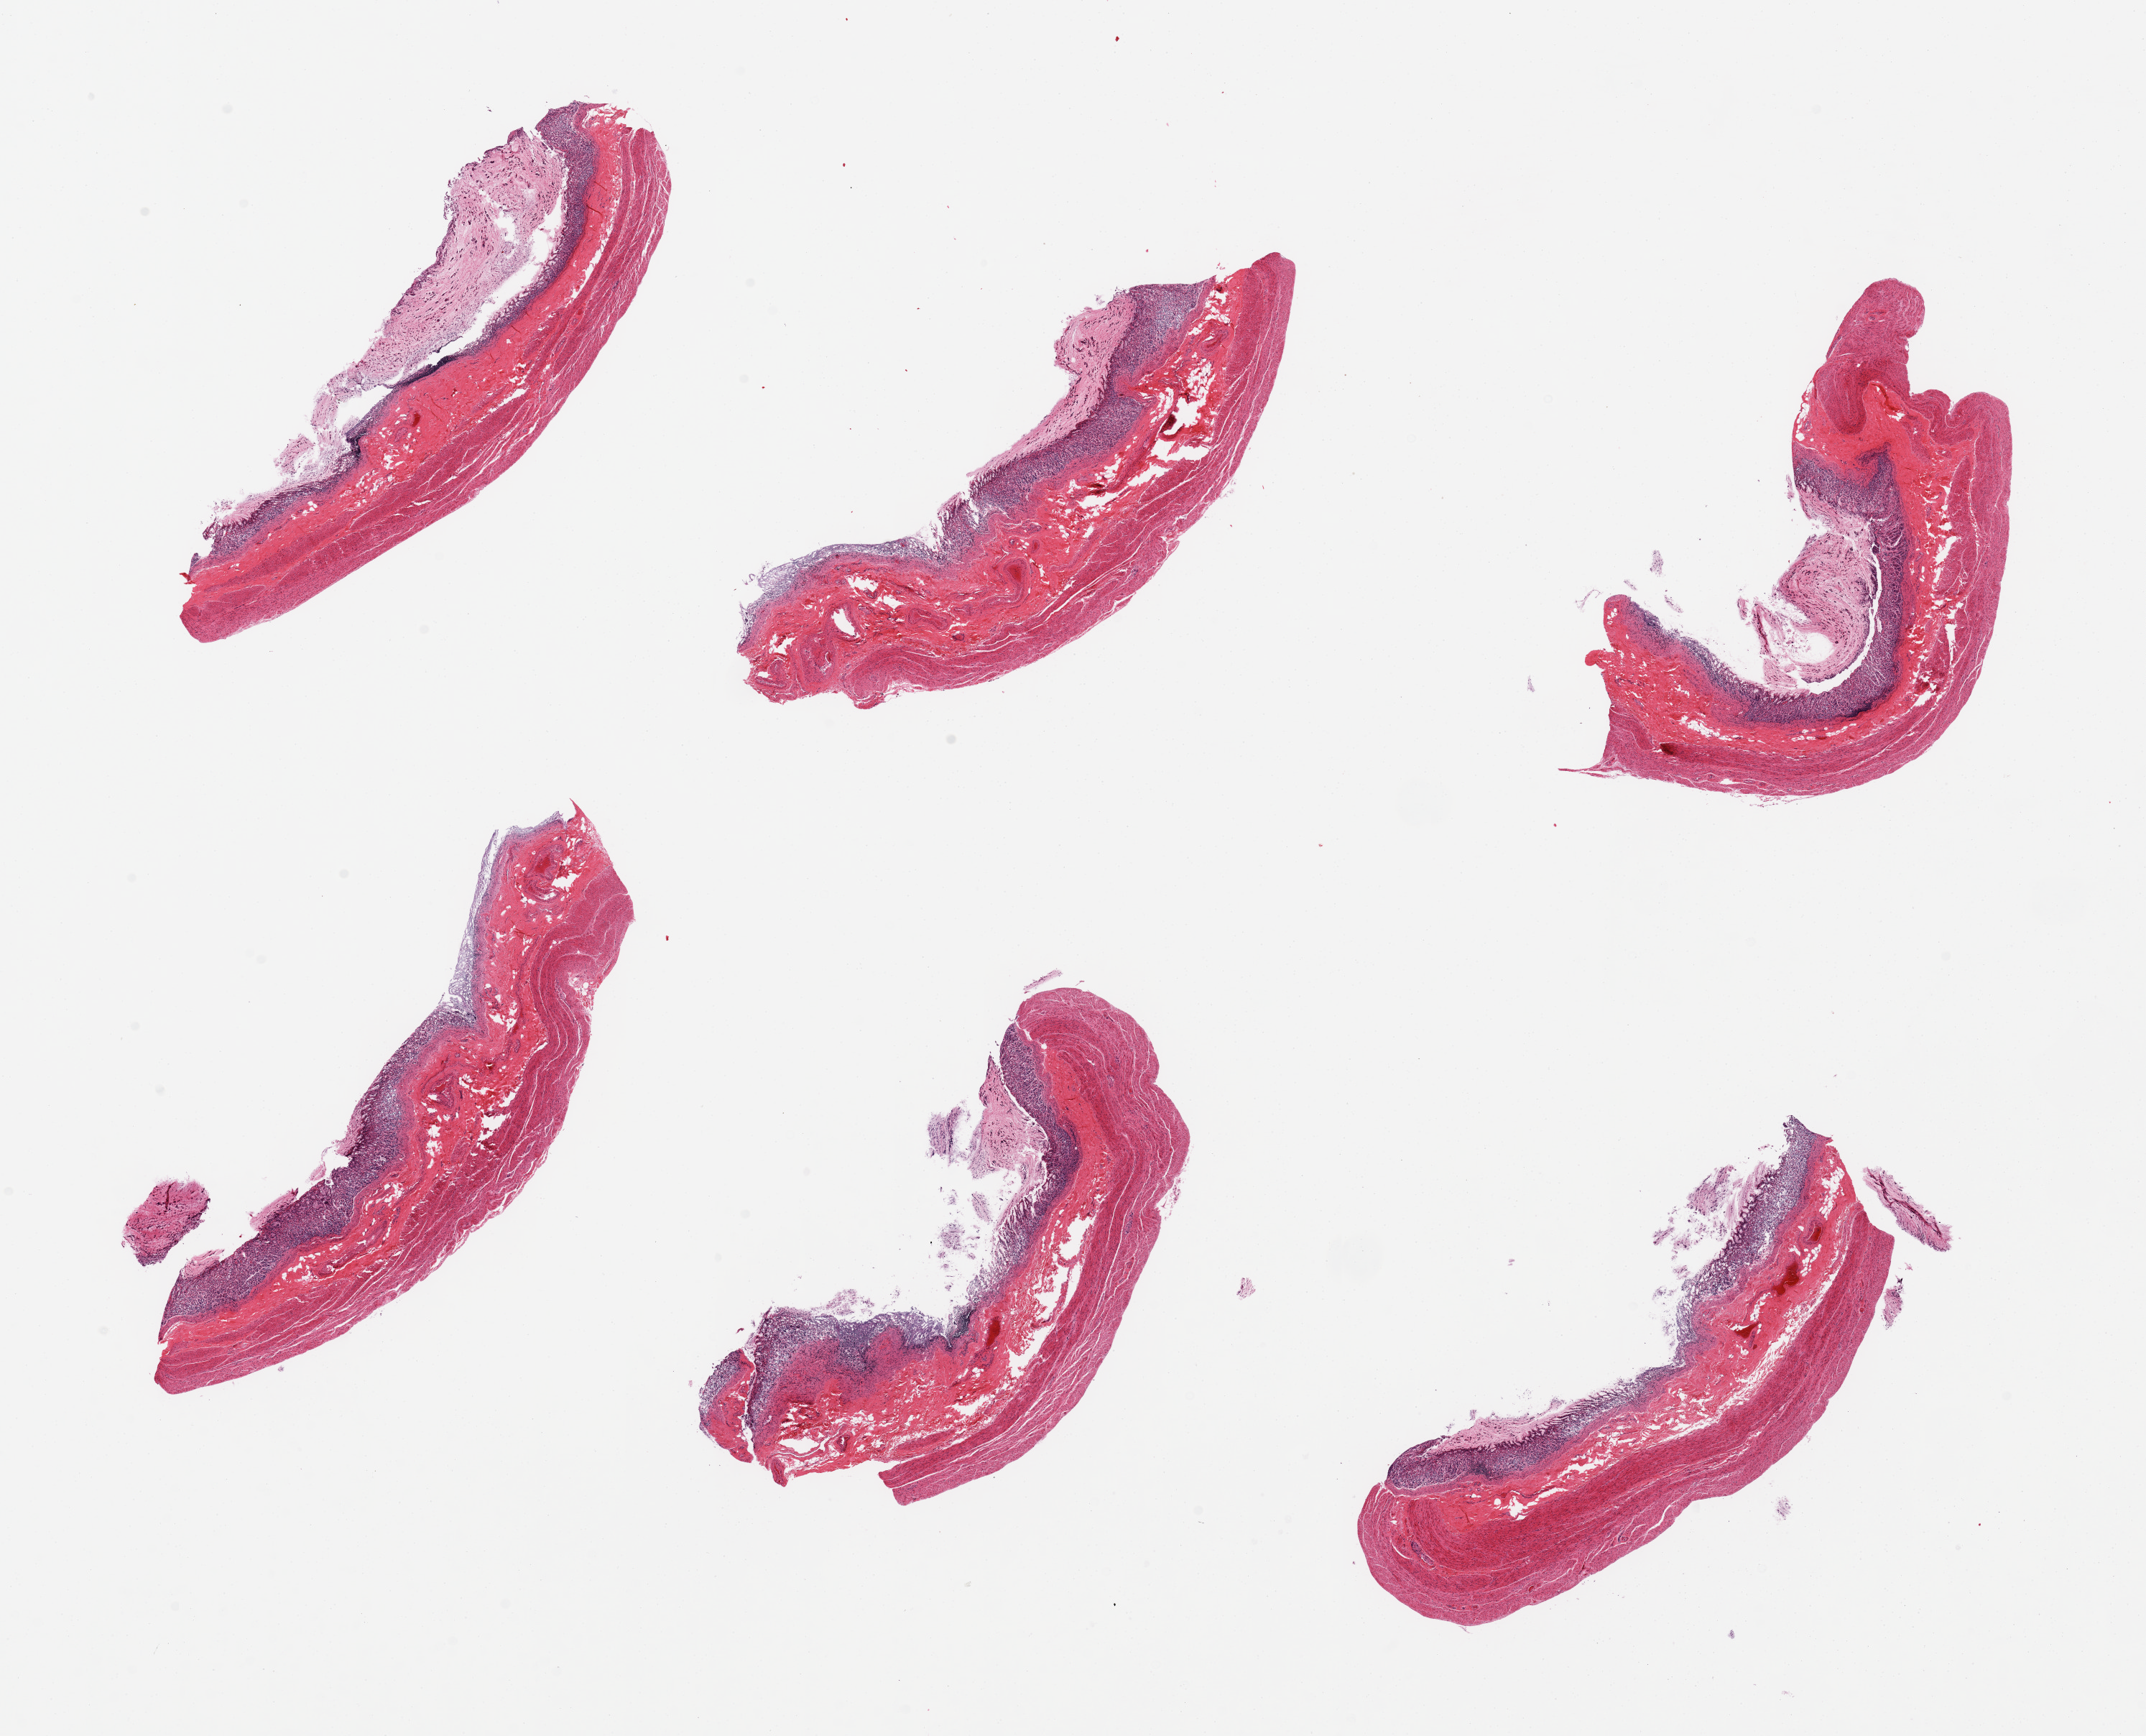
Haematoxylin and eosin whole-slide image, brightfield, a low-resolution overview of the entire scanned area, about 23.6 x 19.1 mm (from a 20x scan); PAXgene-fixed paraffin-embedded (PFPE) section; section of stomach (target tissue); donor tissue sample. Donor: male.
Review note (as recorded): 6 pieces, moderate to generally severe mucosal autolysis.